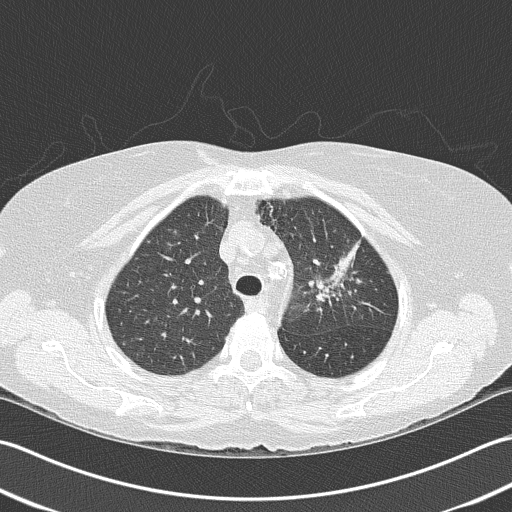
Chest CT (low-dose screening protocol), one axial image; baseline screening round; lung window (W 1500 / L -600 HU); 120 kVp; 512 × 512 image matrix, field of view 350 × 350 mm. Female, age 68 years at enrolment. Former smoker at enrolment.
Expert reader's lesion annotation, bounding box (x1, y1, x2, y2) in pixels: (296, 230, 370, 313). Screening reader's record for this exam: no non-calcified nodule ≥4 mm recorded. Official screen result: negative screen, minor abnormalities not suspicious for lung cancer. Later outcome: lung cancer diagnosed 763 days after this screen (after the third annual screen) — adenocarcinoma, NOS, left upper lobe, poorly differentiated (G3), stage IB (AJCC 6th edition), 50 mm at pathology.